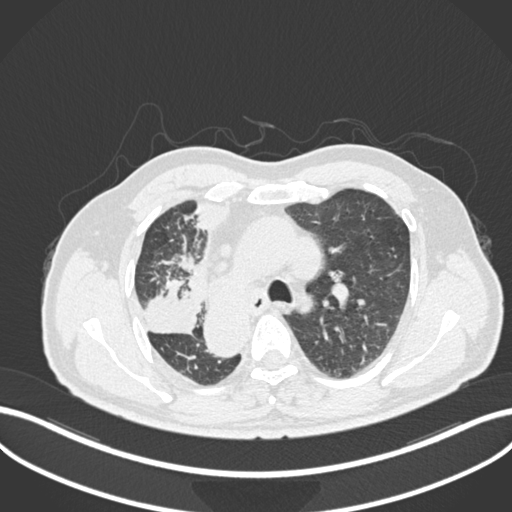
Chest CT, one axial slice; slice 166 of 206 in the series (ordered by position); 120 kVp; lung window (W 1500 / L -600 HU); 1 mm slice thickness; 512 × 512 image matrix. Male patient, age 67 years. Case-level facts recorded for this patient, not image findings: clinical TNM (as recorded): T2a N0 M0.
Outlined on this slice (rectangle marked by the reading radiologist):
- lung tumour (recorded histology: squamous cell carcinoma): bounding box <142,274,200,341> (left, top, right, bottom; pixels)